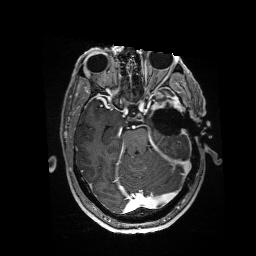
Brain MRI from a brain-tumour surgery series, one axial slice. Position 105 of 176 along the scan axis. T1-weighted post-contrast. 1 mm slice thickness. 256 × 256 image matrix, field of view 256 × 256 mm. Case-level facts recorded for this patient, not image findings: histopathology: Glioblastoma; WHO grade: 4; IDH mutation: no; tumour location: Left Anterior/Superior Temporal.
Structures marked on this image (manually delineated by an expert):
- residual tumour: bounding box <151,93,186,114> (left, top, right, bottom; pixels)